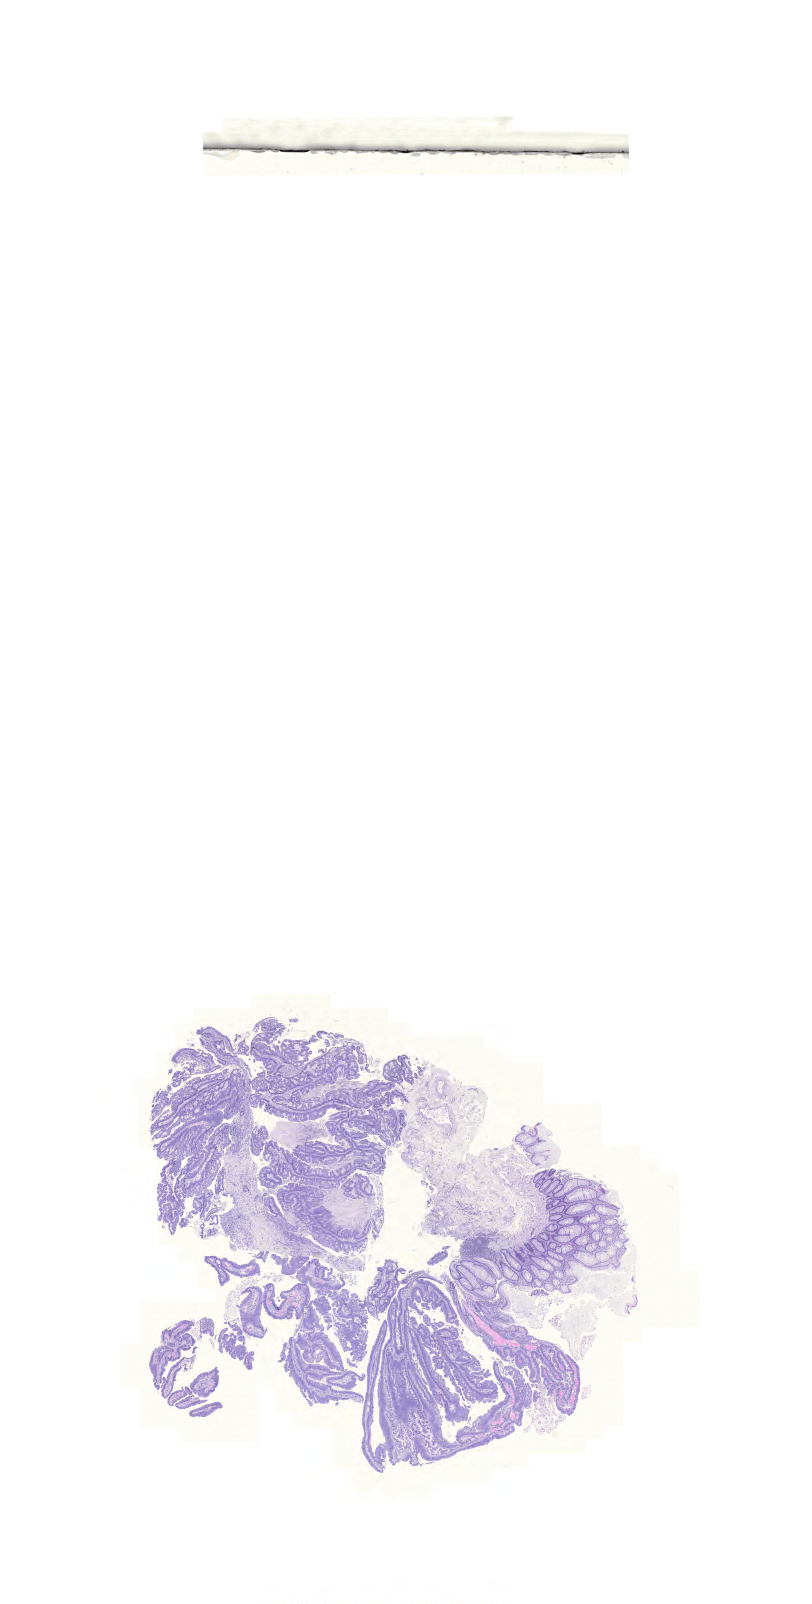
Digitized H&E-stained tissue section (whole slide), whole scanned area (about 12.1 x 23.9 mm, from a 20x scan) shown as a low-resolution overview, formalin-fixed paraffin-embedded (FFPE) diagnostic section, primary tumour sample from the colon. Male patient; age at initial diagnosis 64 years.
AJCC pathologic stage: IIA. Diagnosis: Adenocarcinoma, NOS (descending colon).